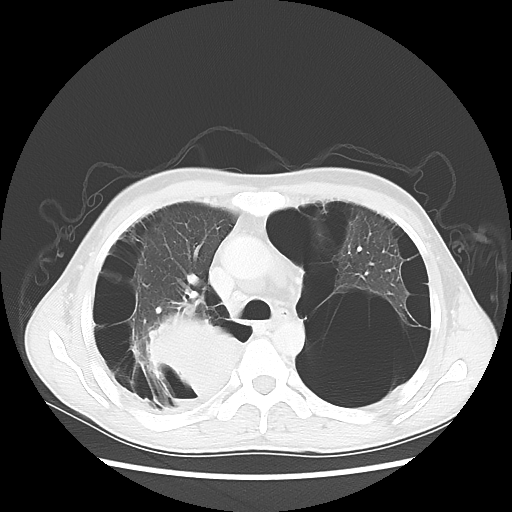
Chest CT, one axial slice. Reconstruction kernel LUNG. 140 kVp. Lung window (W 1500 / L -600 HU). 5 mm slice thickness. 512 × 512 image matrix, field of view 351 × 351 mm. Patient: male, 41 years. Case-level facts recorded for this patient, not image findings: clinical TNM (as recorded): T4 N0 M1a.
Outlined on this slice (bounding box drawn by a radiologist):
- lung tumour (recorded histology: large cell carcinoma): box from (x=135, y=306) to (x=240, y=404) px